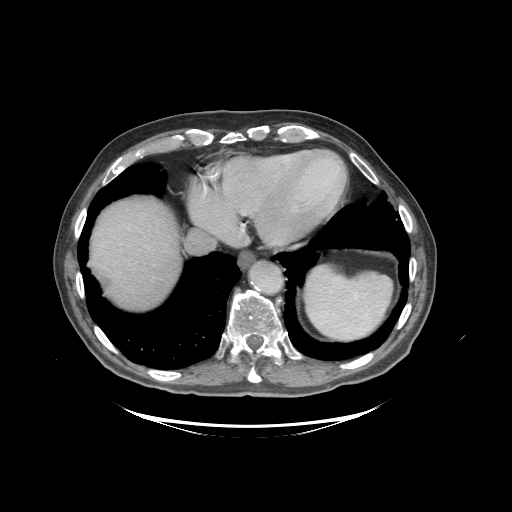
Contrast-enhanced abdominal CT (liver protocol), one axial slice. Position 86 of 99 along the scan axis. Reconstruction kernel STANDARD. Soft-tissue window (W 400 / L 40 HU). 2.5 mm slice thickness. 512 × 512 image matrix, field of view 460 × 460 mm. From the clinical record (not read from this slice): diagnosis: hepatocellular carcinoma (patient treated with transarterial chemoembolisation; whether this scan precedes or follows treatment is not stated here); TNM stage (as recorded): Stage-I; Child-Pugh class: A; tumour differentiation: moderately differentiated.
Annotated regions visible in this slice (semi-automatically segmented with operator editing):
- abdominal aorta: bounding box (x1, y1, x2, y2) in pixels: (252, 264, 282, 293)
- liver parenchyma outside the tumour (the mass and vessels are separate outlines, so this box may not span the whole liver): (90, 198, 180, 308)